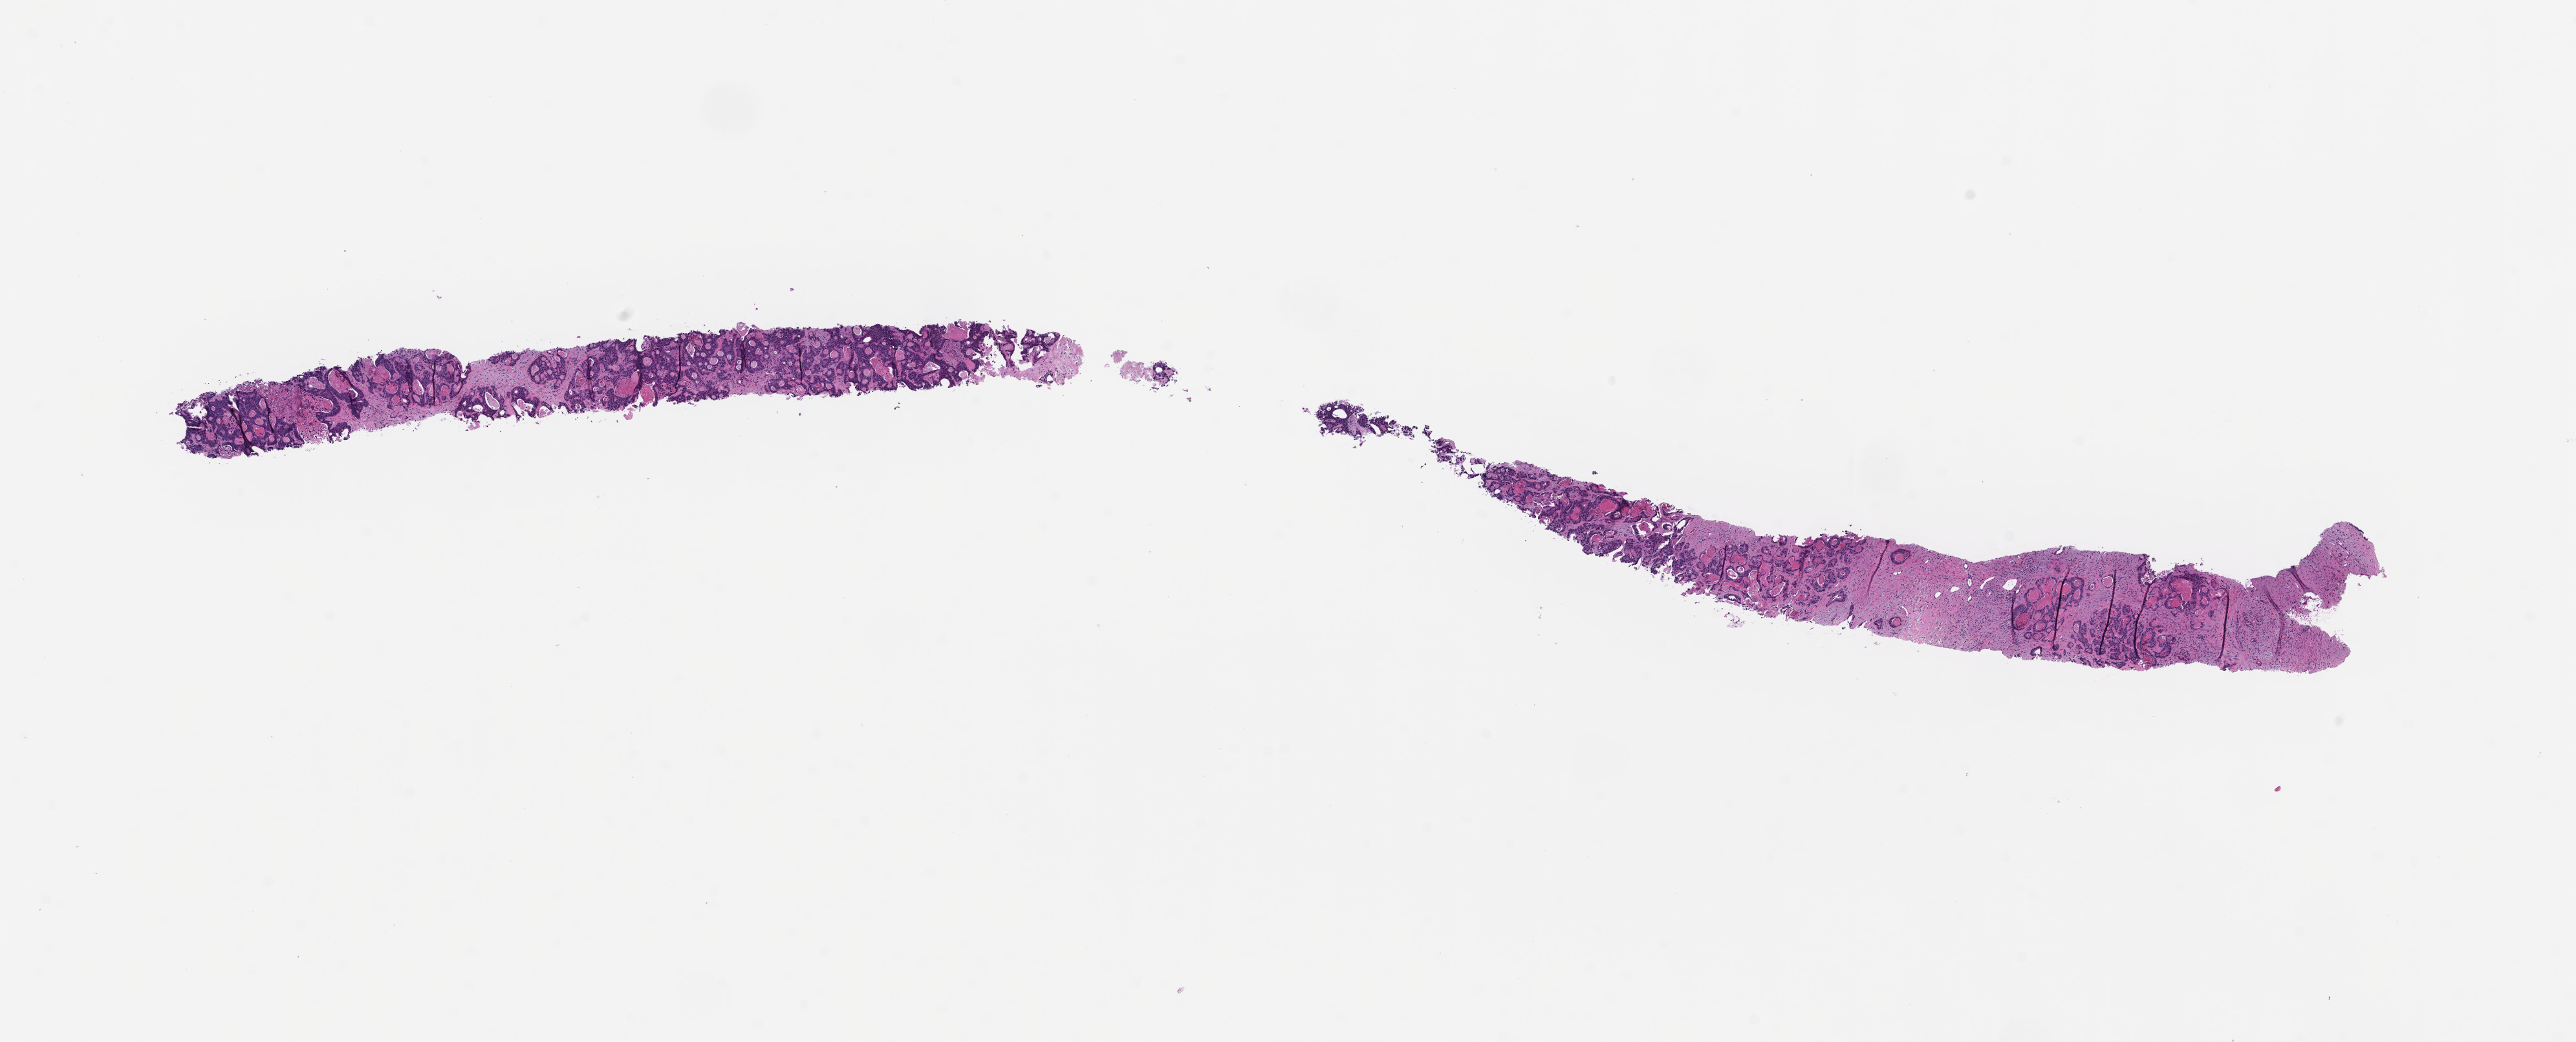
Digitized haematoxylin and eosin-stained section, low-resolution overview of the scanned area, about 16.1 x 6.5 mm; formalin-fixed, paraffin-embedded (FFPE) tissue; specimen time point: collected at disease progression. Male patient.
This section: metastasis (sampled organ not recorded). Primary diagnosis of the patient: Colorectal Carcinoma.